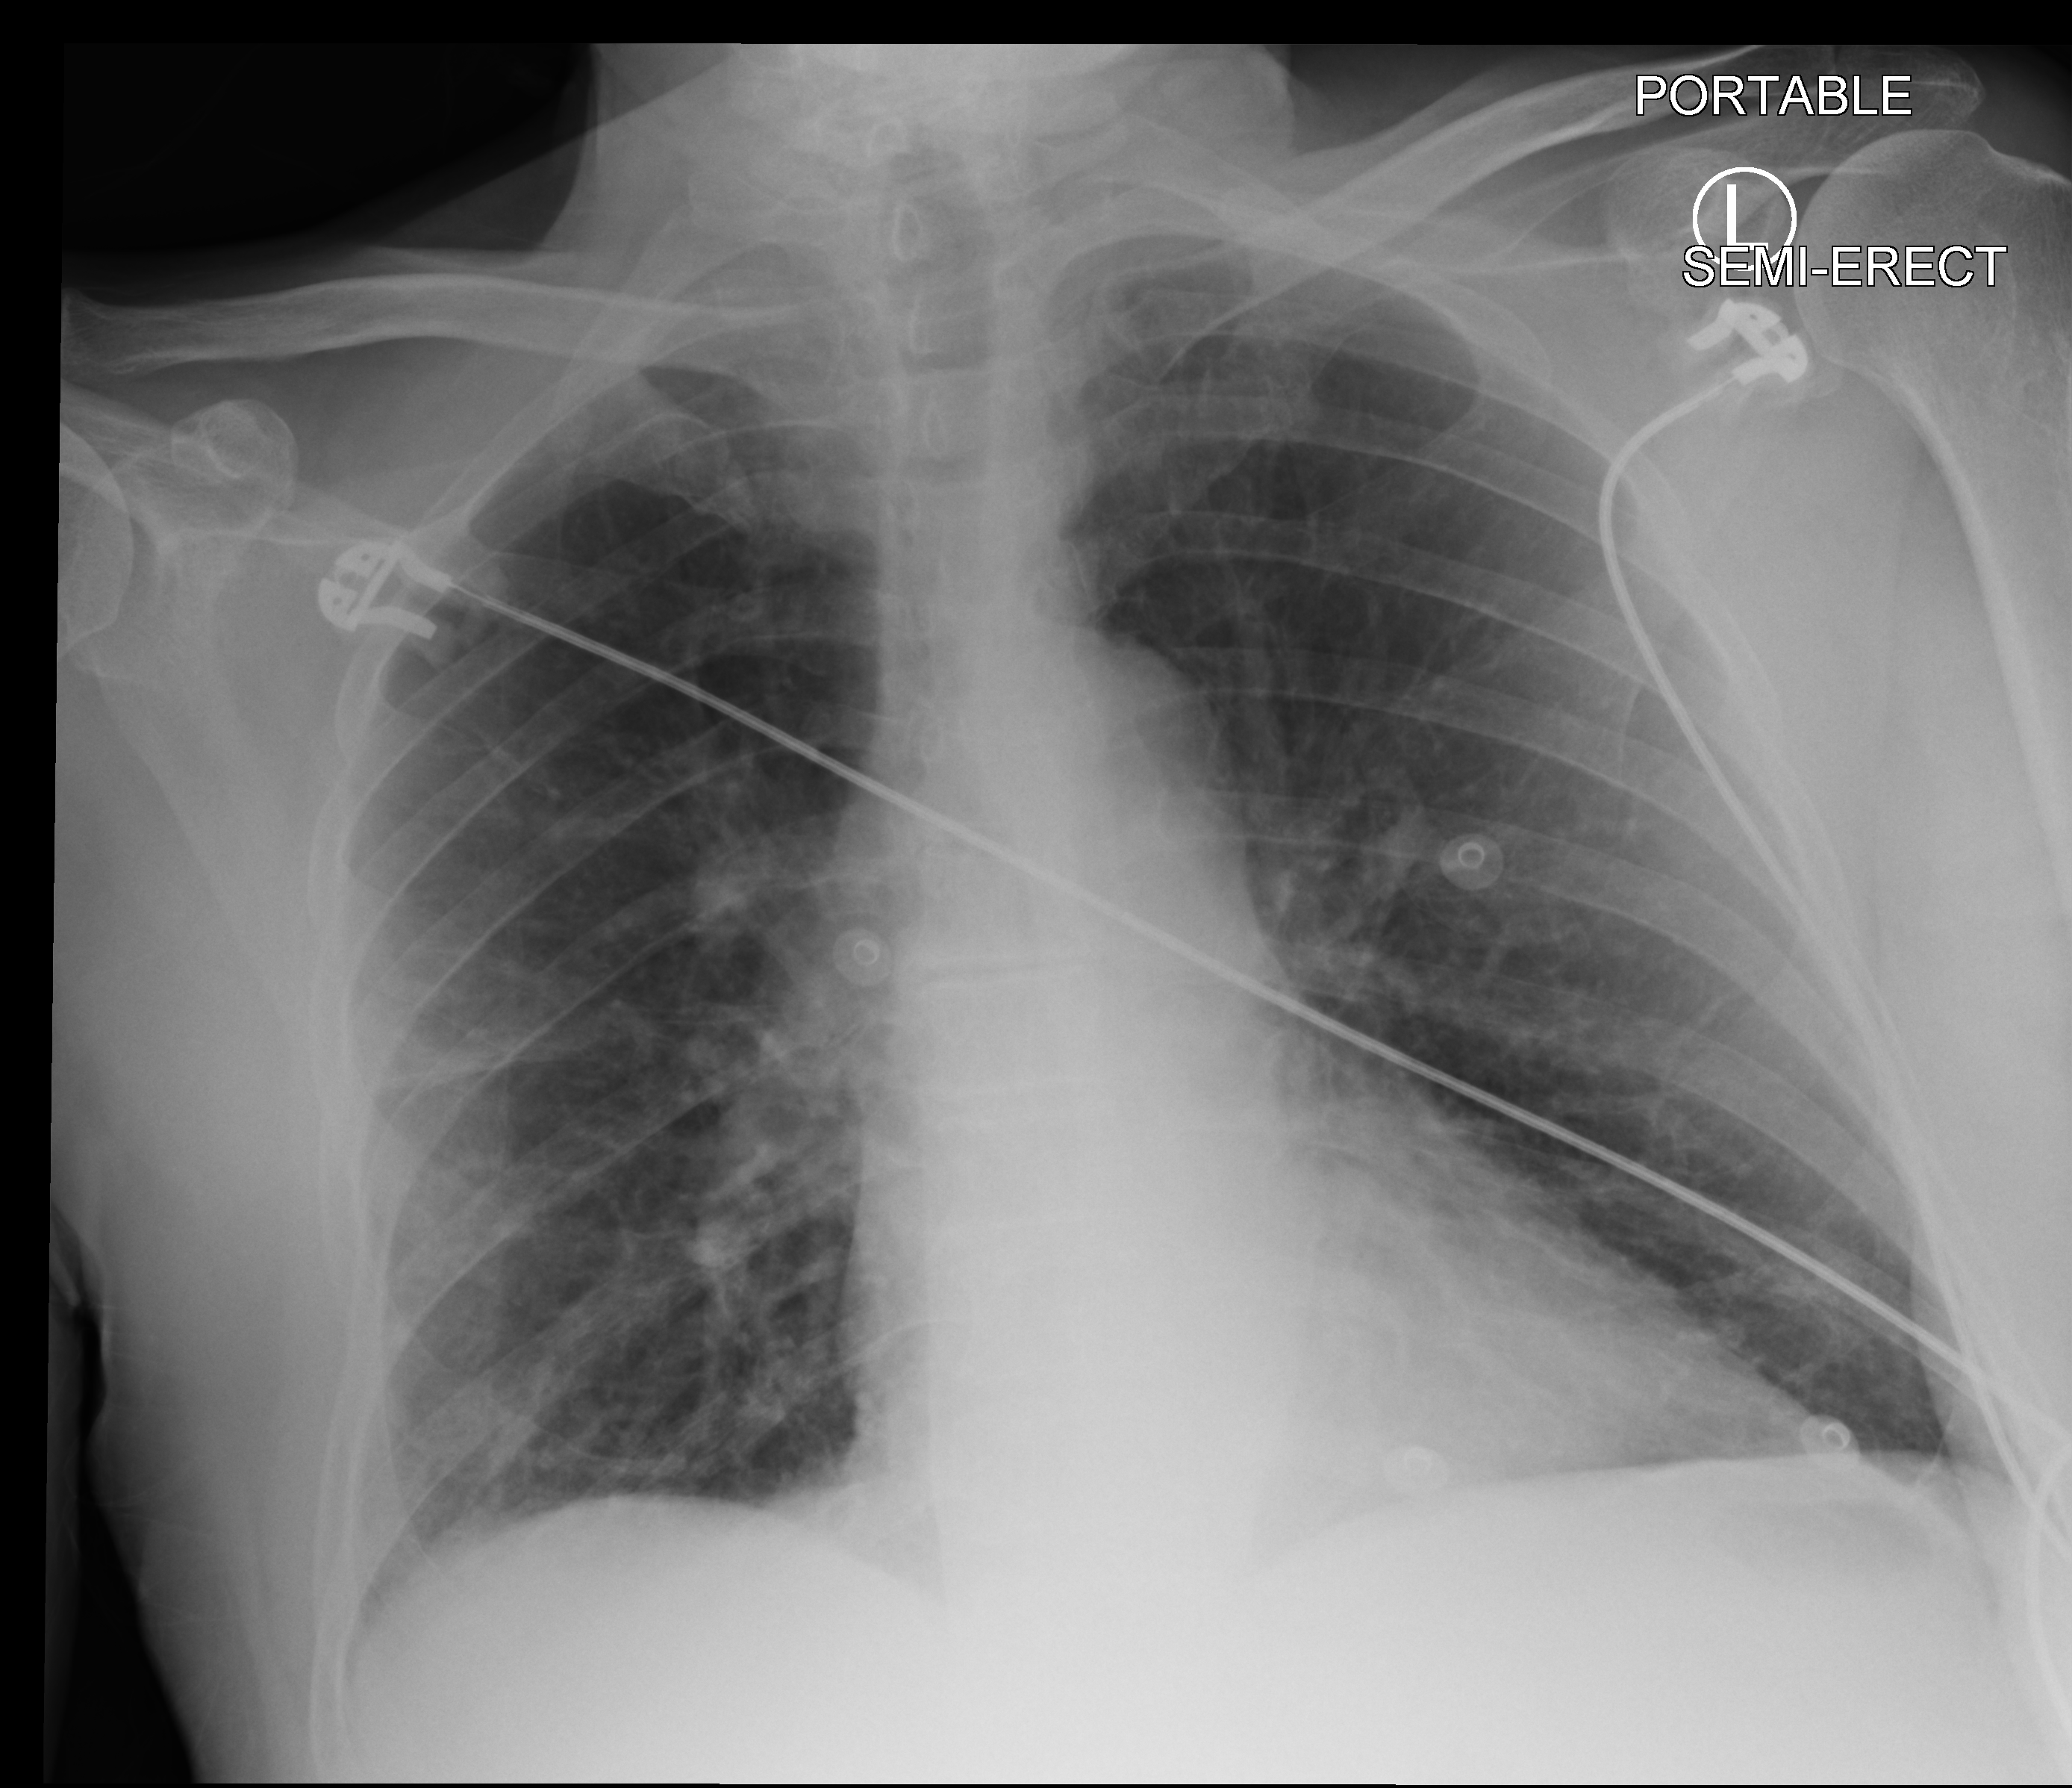
Chest X-ray (portable). Patient hospitalised with COVID-19; male, aged 75–90 years.
Hospital-stay facts (about this admission, not read from this image; timing relative to this image not recorded):
- length of hospital stay: 70 days